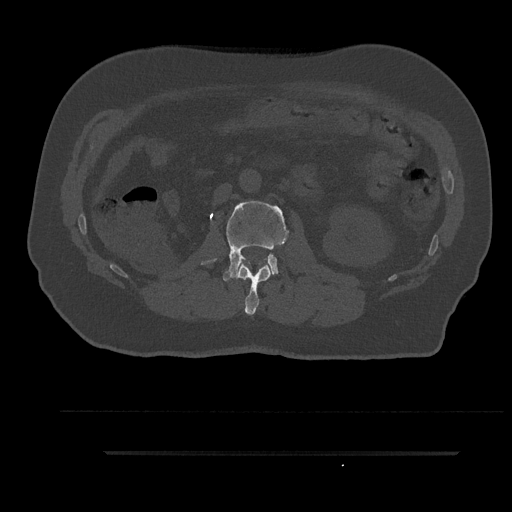
CT including the spine, one axial slice. Position 133 of 797 along the scan axis. 120 kVp. Bone window (W 1800 / L 400 HU). 0.5 mm slice thickness. 512 × 512 image matrix, field of view 432 × 432 mm. Patient: male, 63 years. From the clinical record (not read from this slice): primary cancer: renal.
Structures marked on this image (semi-automatic segmentation, software-assisted and operator-edited):
- L1 vertebra: box from (x=234, y=262) to (x=271, y=315) px
- L2 vertebra: (x=202, y=201)–(x=289, y=281)